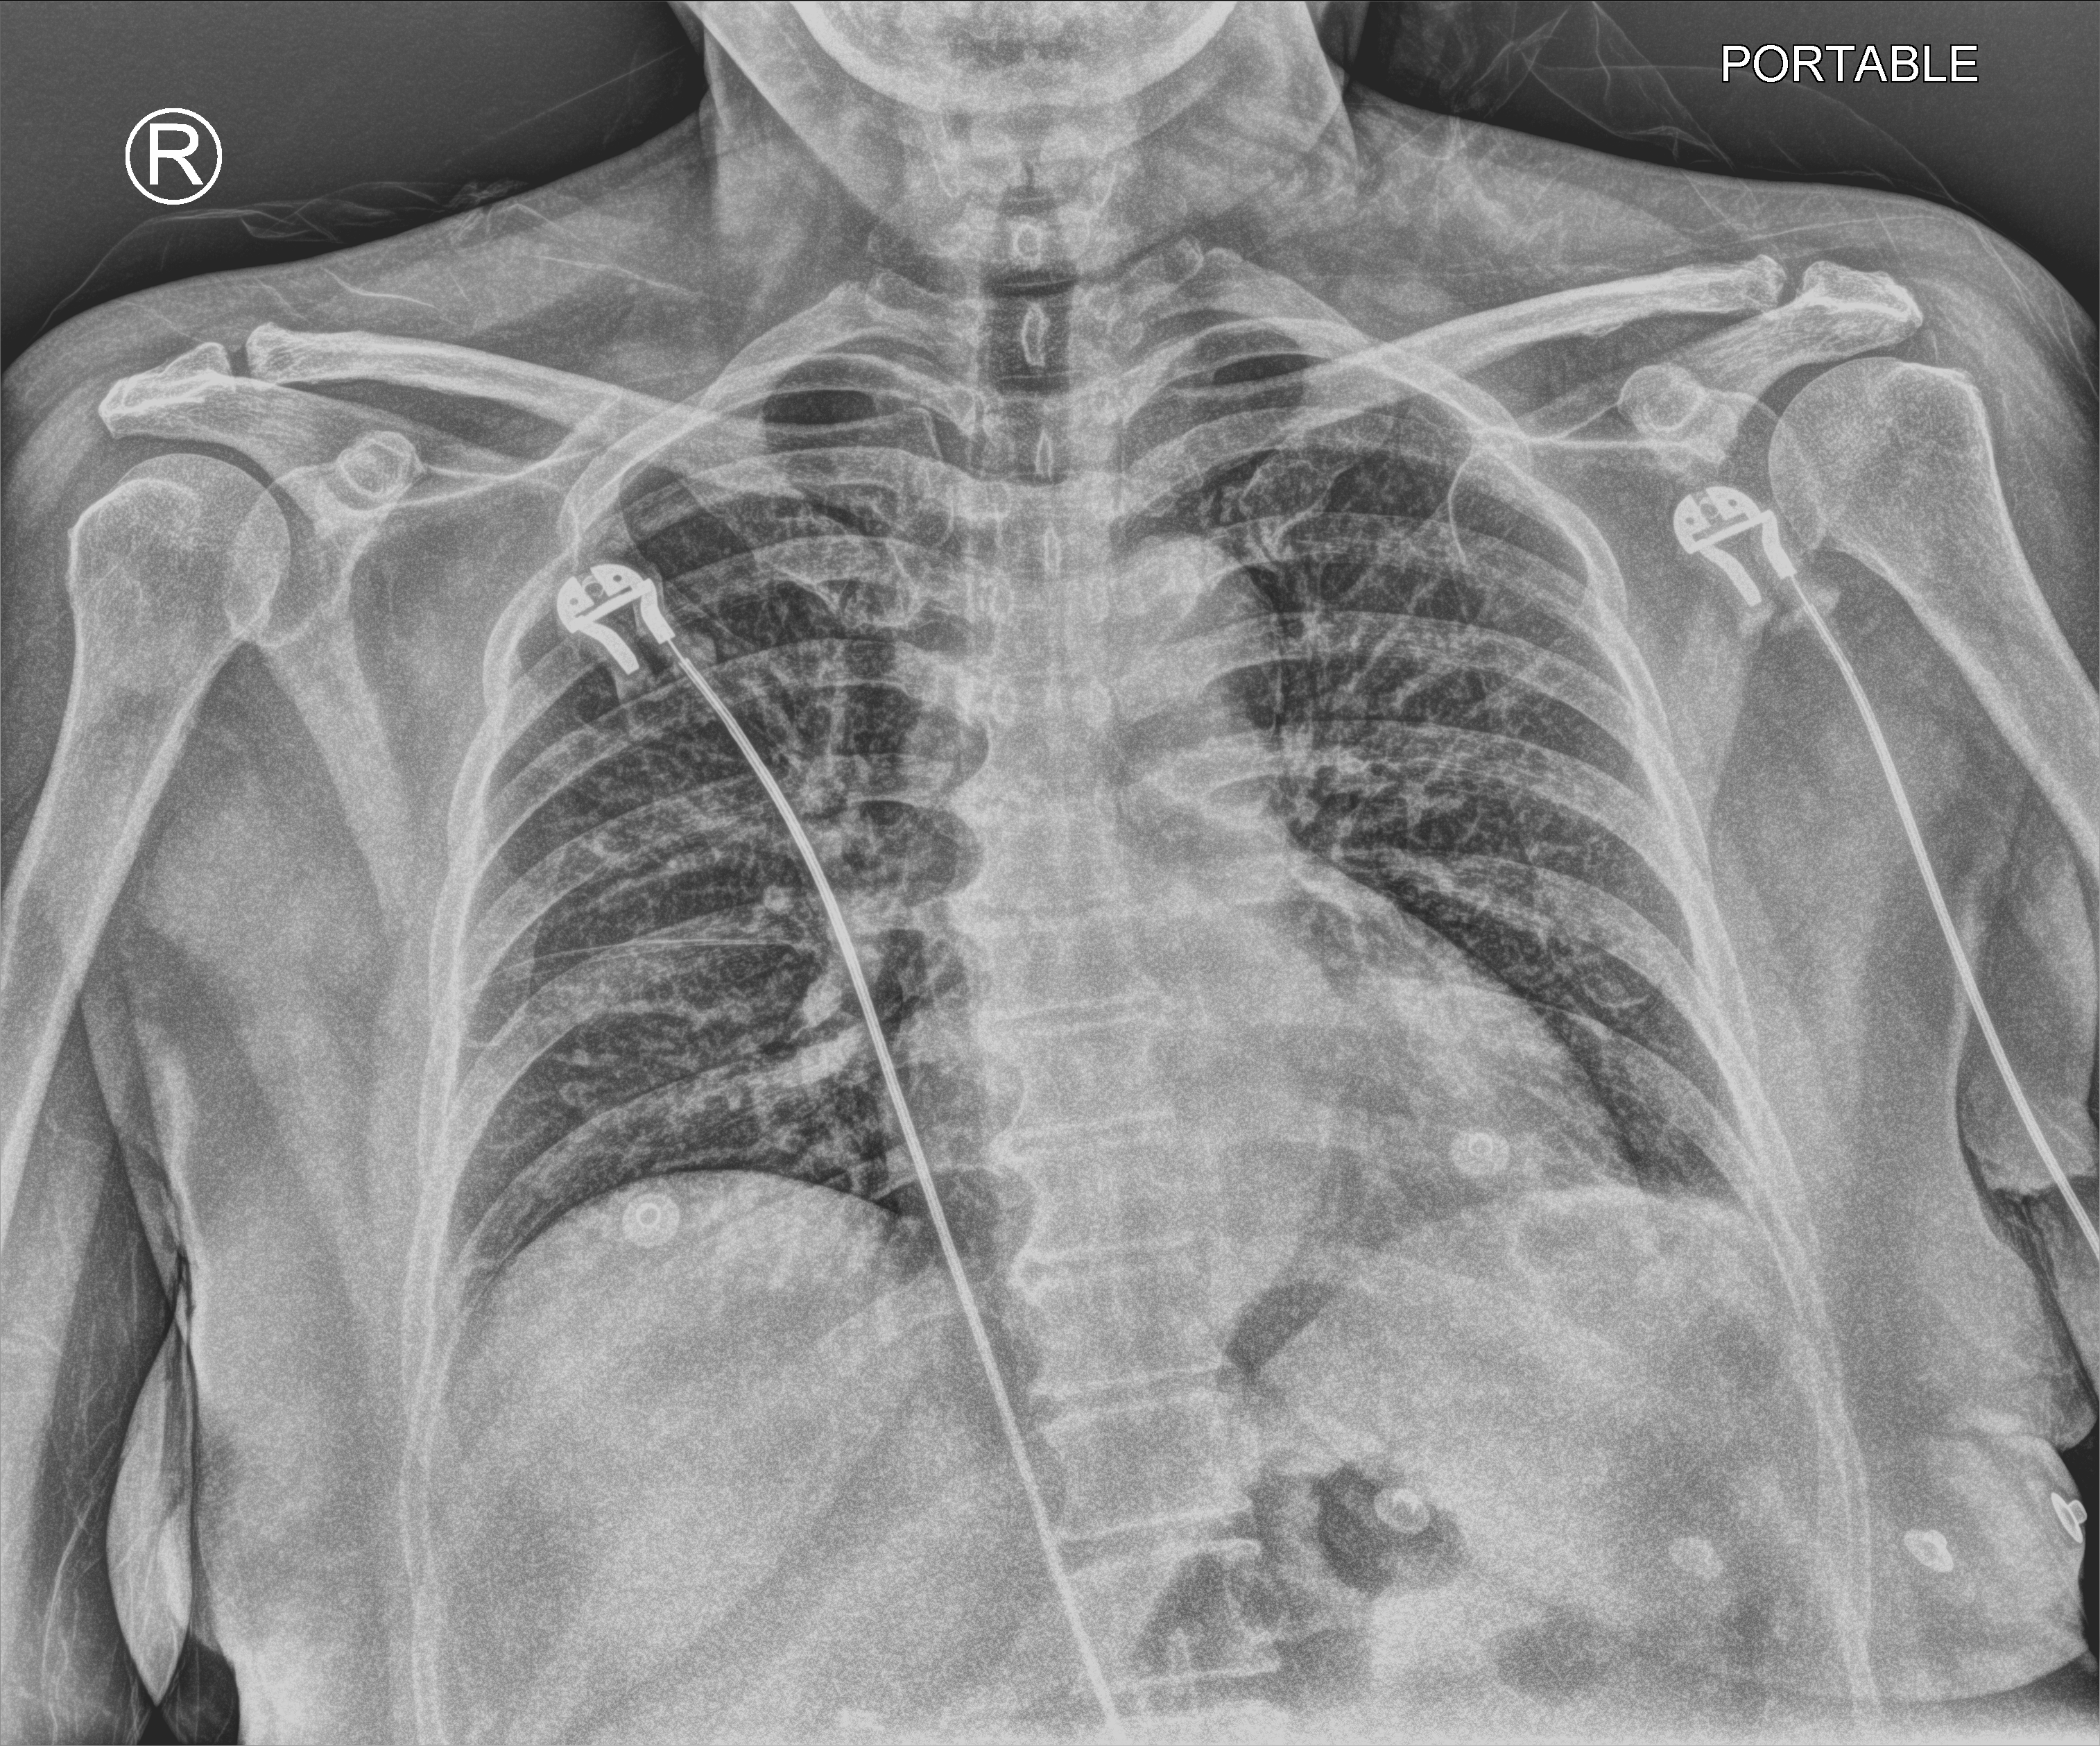
Portable chest radiograph, anteroposterior (AP) projection. Female patient hospitalised with COVID-19, age 18–59 years.
From the hospital-stay record, not from the radiograph (when in the stay this image was taken is not recorded): mechanically ventilated during this hospital stay: no; diabetes (admission record): no.